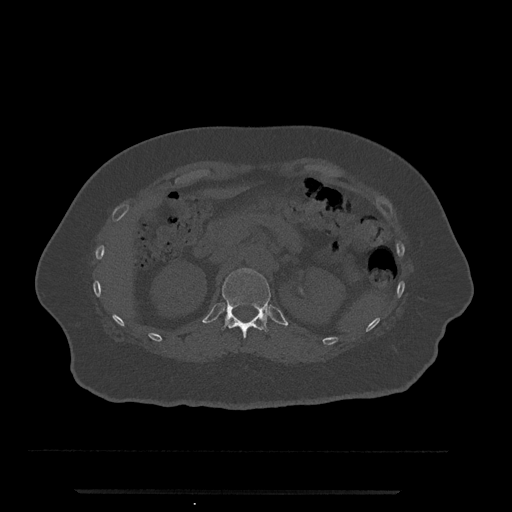
CT including the spine, one axial slice; 120 kVp; bone window (W 1800 / L 400 HU); 0.5 mm slice thickness; 512 × 512 image matrix, field of view 440 × 440 mm. Patient: female, 51 years. From the clinical record (not read from this slice): primary cancer: neuro; vertebrae with lytic lesions (as recorded): T8.
Structures marked on this image (semi-automatically segmented with operator editing):
- T12 vertebra: box from (x=222, y=268) to (x=271, y=338) px